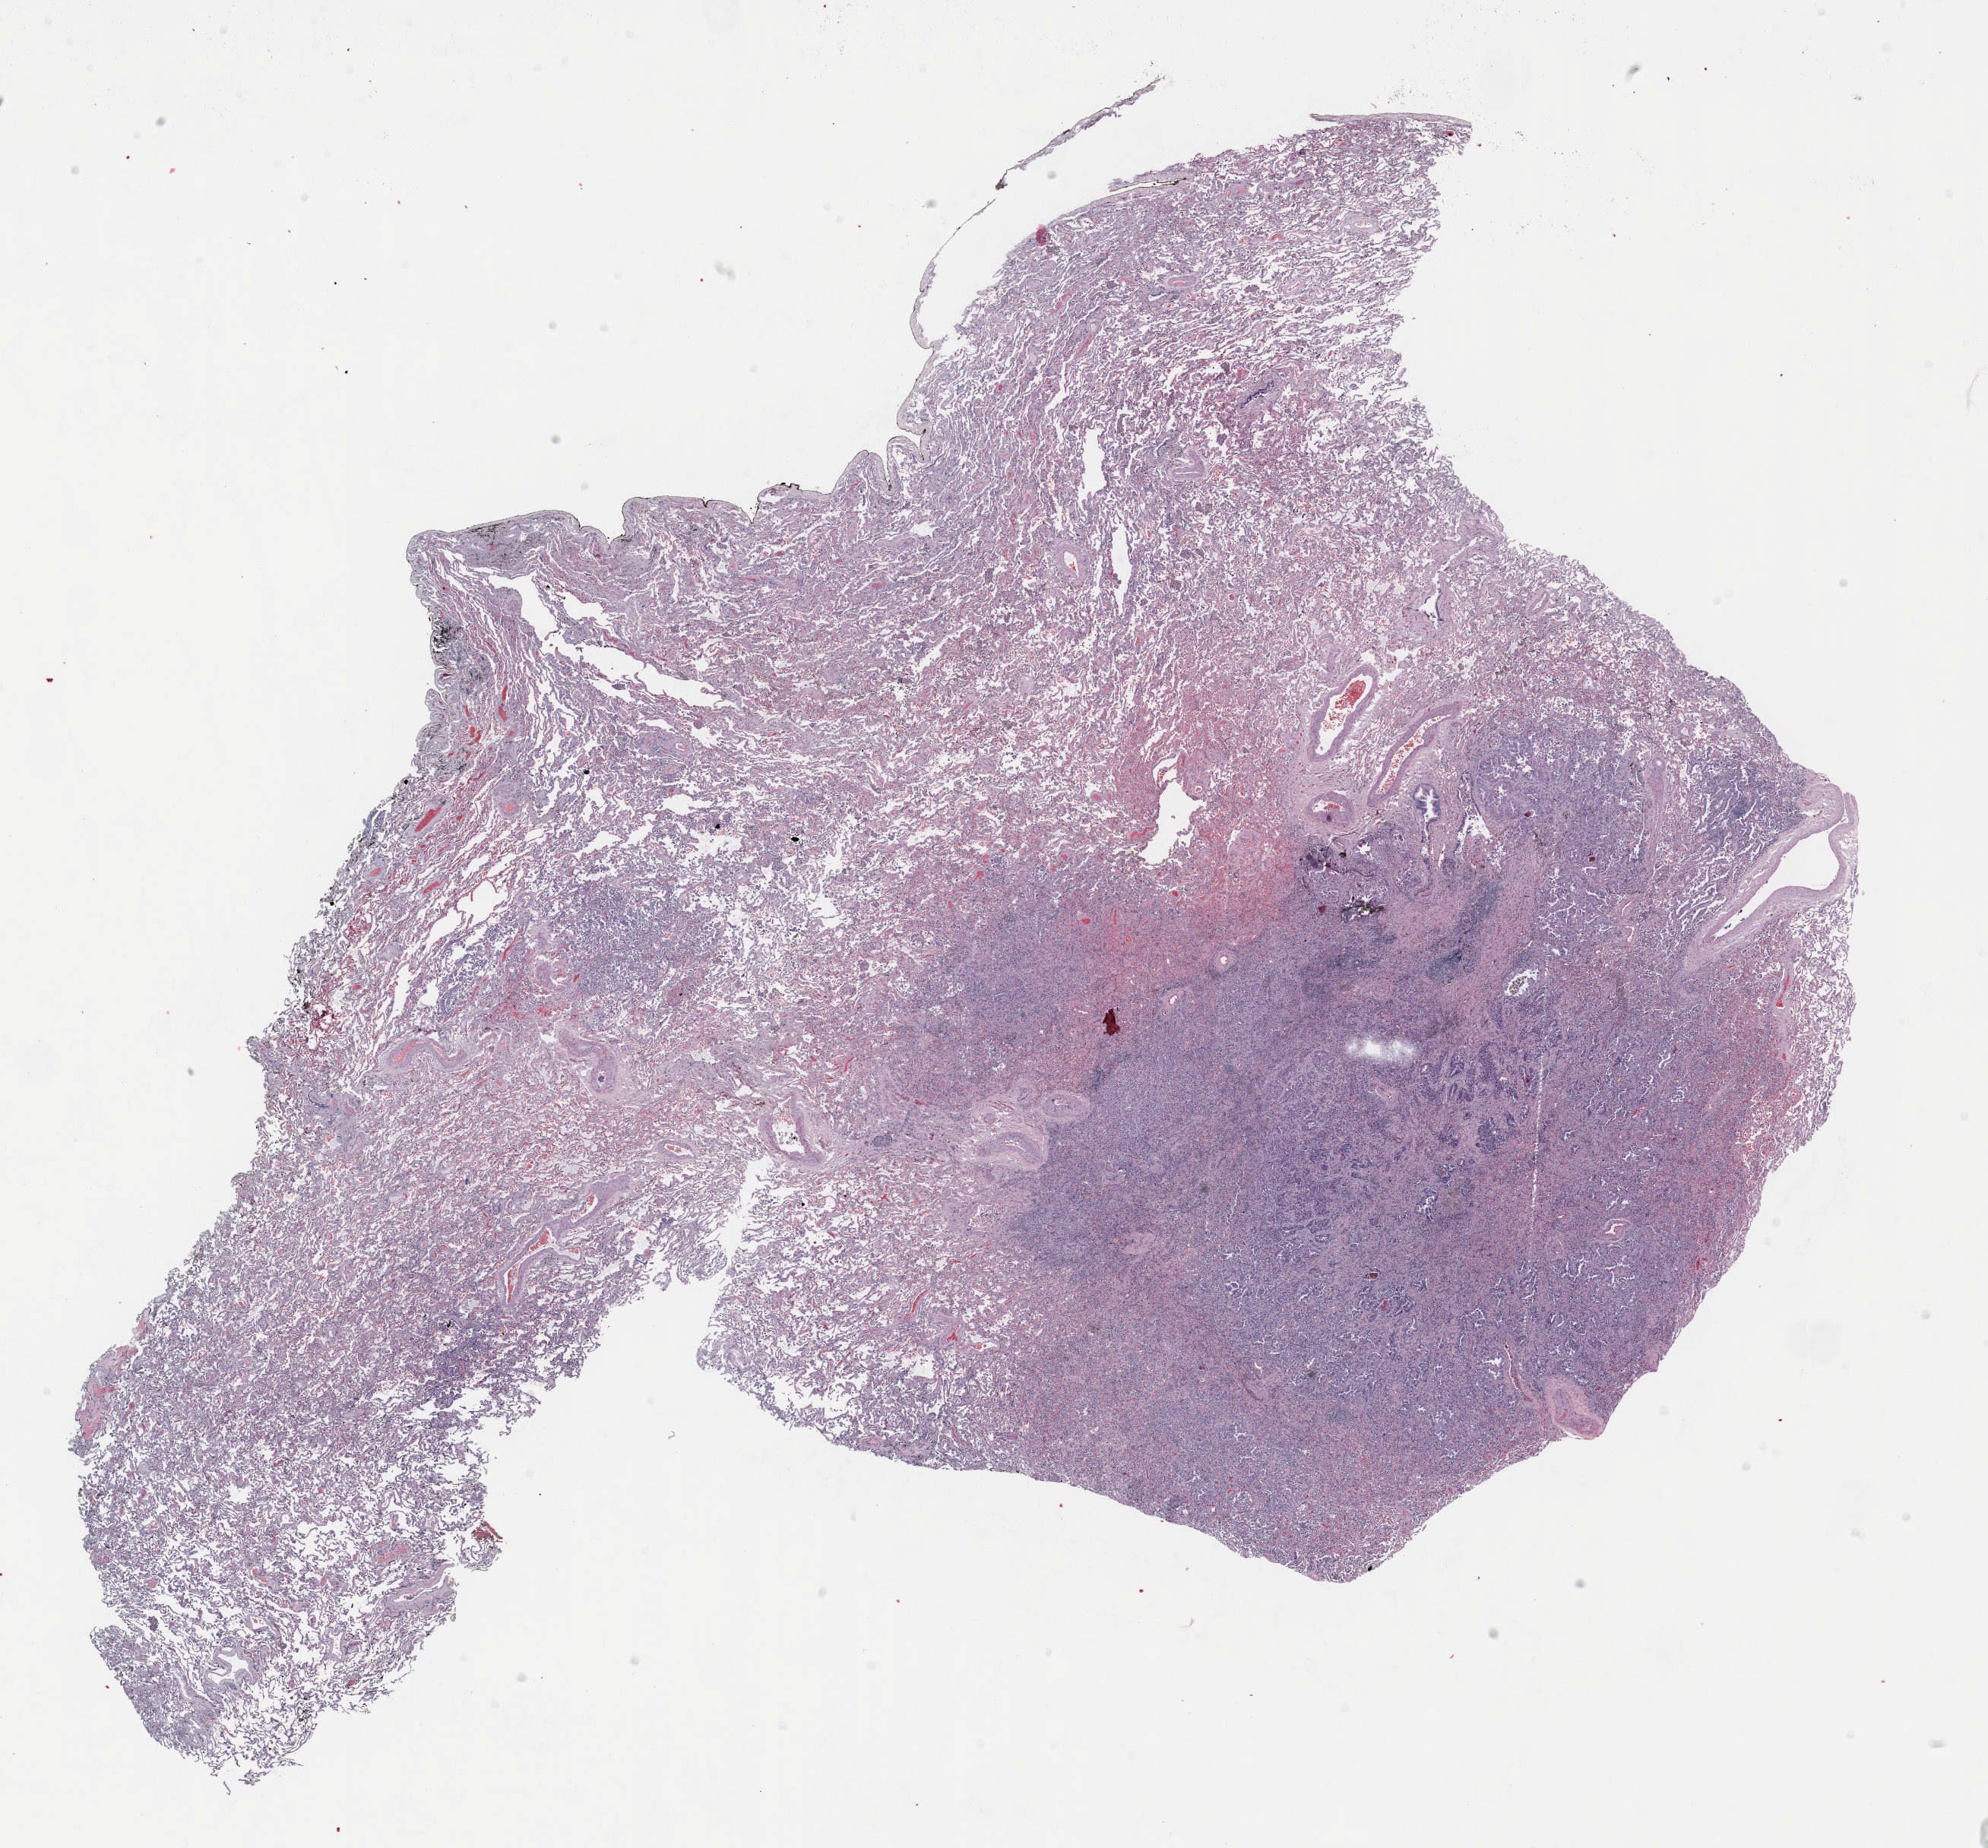
Hematoxylin and eosin (H&E) stained whole-slide image — shown as a low-resolution overview of the whole scanned area (about 21.0 x 19.5 mm, acquisition: 20x scan), formalin-fixed paraffin-embedded (FFPE) section, lung tissue. Female, age 57 at enrolment. Grade: moderately differentiated (G2).
* tumour size (pathology): 15 mm
* stage (AJCC 6th edition): IA
* primary tumour location (clinical record): right upper lobe
* participant's lung-cancer diagnosis: Adenocarcinoma, NOS